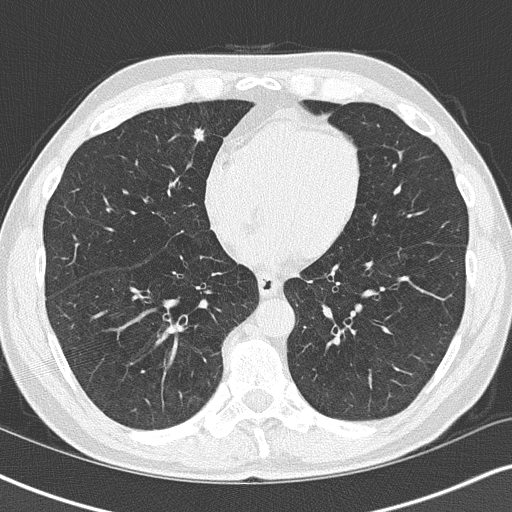
Axial slice from a low-dose chest CT screening exam, second annual screen, lung window (W 1500 / L -600 HU), 2 mm slice thickness, lung (sharp) reconstruction kernel (B50f), slice 105 of 148 in the series. Male, age 58 years at enrolment.
- Expert-annotated lung lesion, bounding box <169,115,222,159> (left, top, right, bottom; pixels).
- Reader record for this screening exam (exam-level; its link to the box is not recorded): non-calcified nodule or mass ≥4 mm, right middle lobe, 8 × 8 mm, spiculated (stellate) margins, soft tissue attenuation, pre-existing on the prior screen: yes; interval growth: yes.